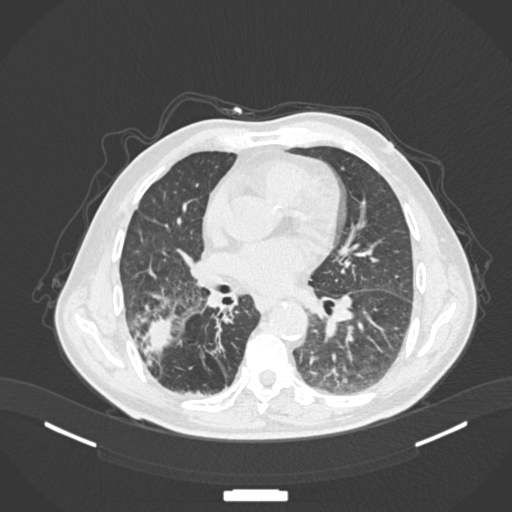
Chest CT, one axial slice; slice 75 of 201 in the series (ordered by position); lung window (W 1500 / L -600 HU); 1 mm slice thickness; 512 × 512 image matrix. Male patient, age 72 years. Case-level facts recorded for this patient, not image findings: clinical TNM (as recorded): T3 N2 M0.
Structures marked on this image (bounding box drawn by a radiologist):
- lung tumour (recorded histology: adenocarcinoma): bounding box [x1, y1, x2, y2] px = [139, 311, 178, 357]